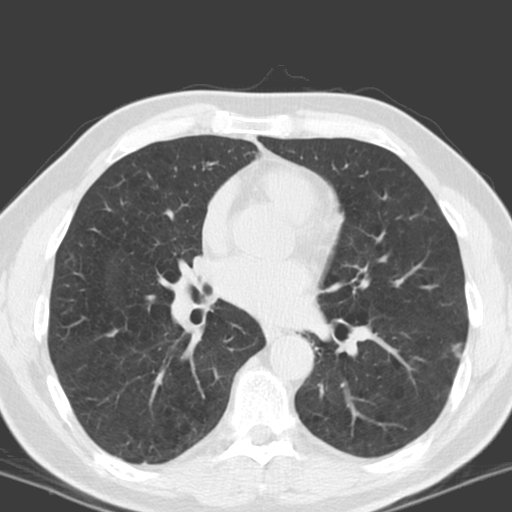
Low-dose screening chest CT, axial slice. Baseline annual screen. Lung window (W 1500 / L -600 HU). 3.2 mm slice thickness. 512 × 512 image matrix, field of view 330 × 330 mm. Male participant, aged 57 years at enrolment. Former smoker at enrolment.
Lesion marked by an expert reader, bounding box <440,329,482,366> (left, top, right, bottom; pixels). Screening reader's record for this exam (one nodule recorded; not confirmed to be the boxed lesion): non-calcified nodule or mass ≥4 mm, left lower lobe, 8 × 5 mm, poorly defined margins, ground glass attenuation. Official screen result: positive, change unspecified: nodule(s) >= 4 mm or enlarging nodule(s), mass(es), or other non-specific abnormalities suspicious for lung cancer. Participant outcome: lung cancer diagnosed 816 days after this screen (after the third annual screen) — non-small cell carcinoma, left lower lobe, stage IV (AJCC 6th edition), 13 mm at pathology.